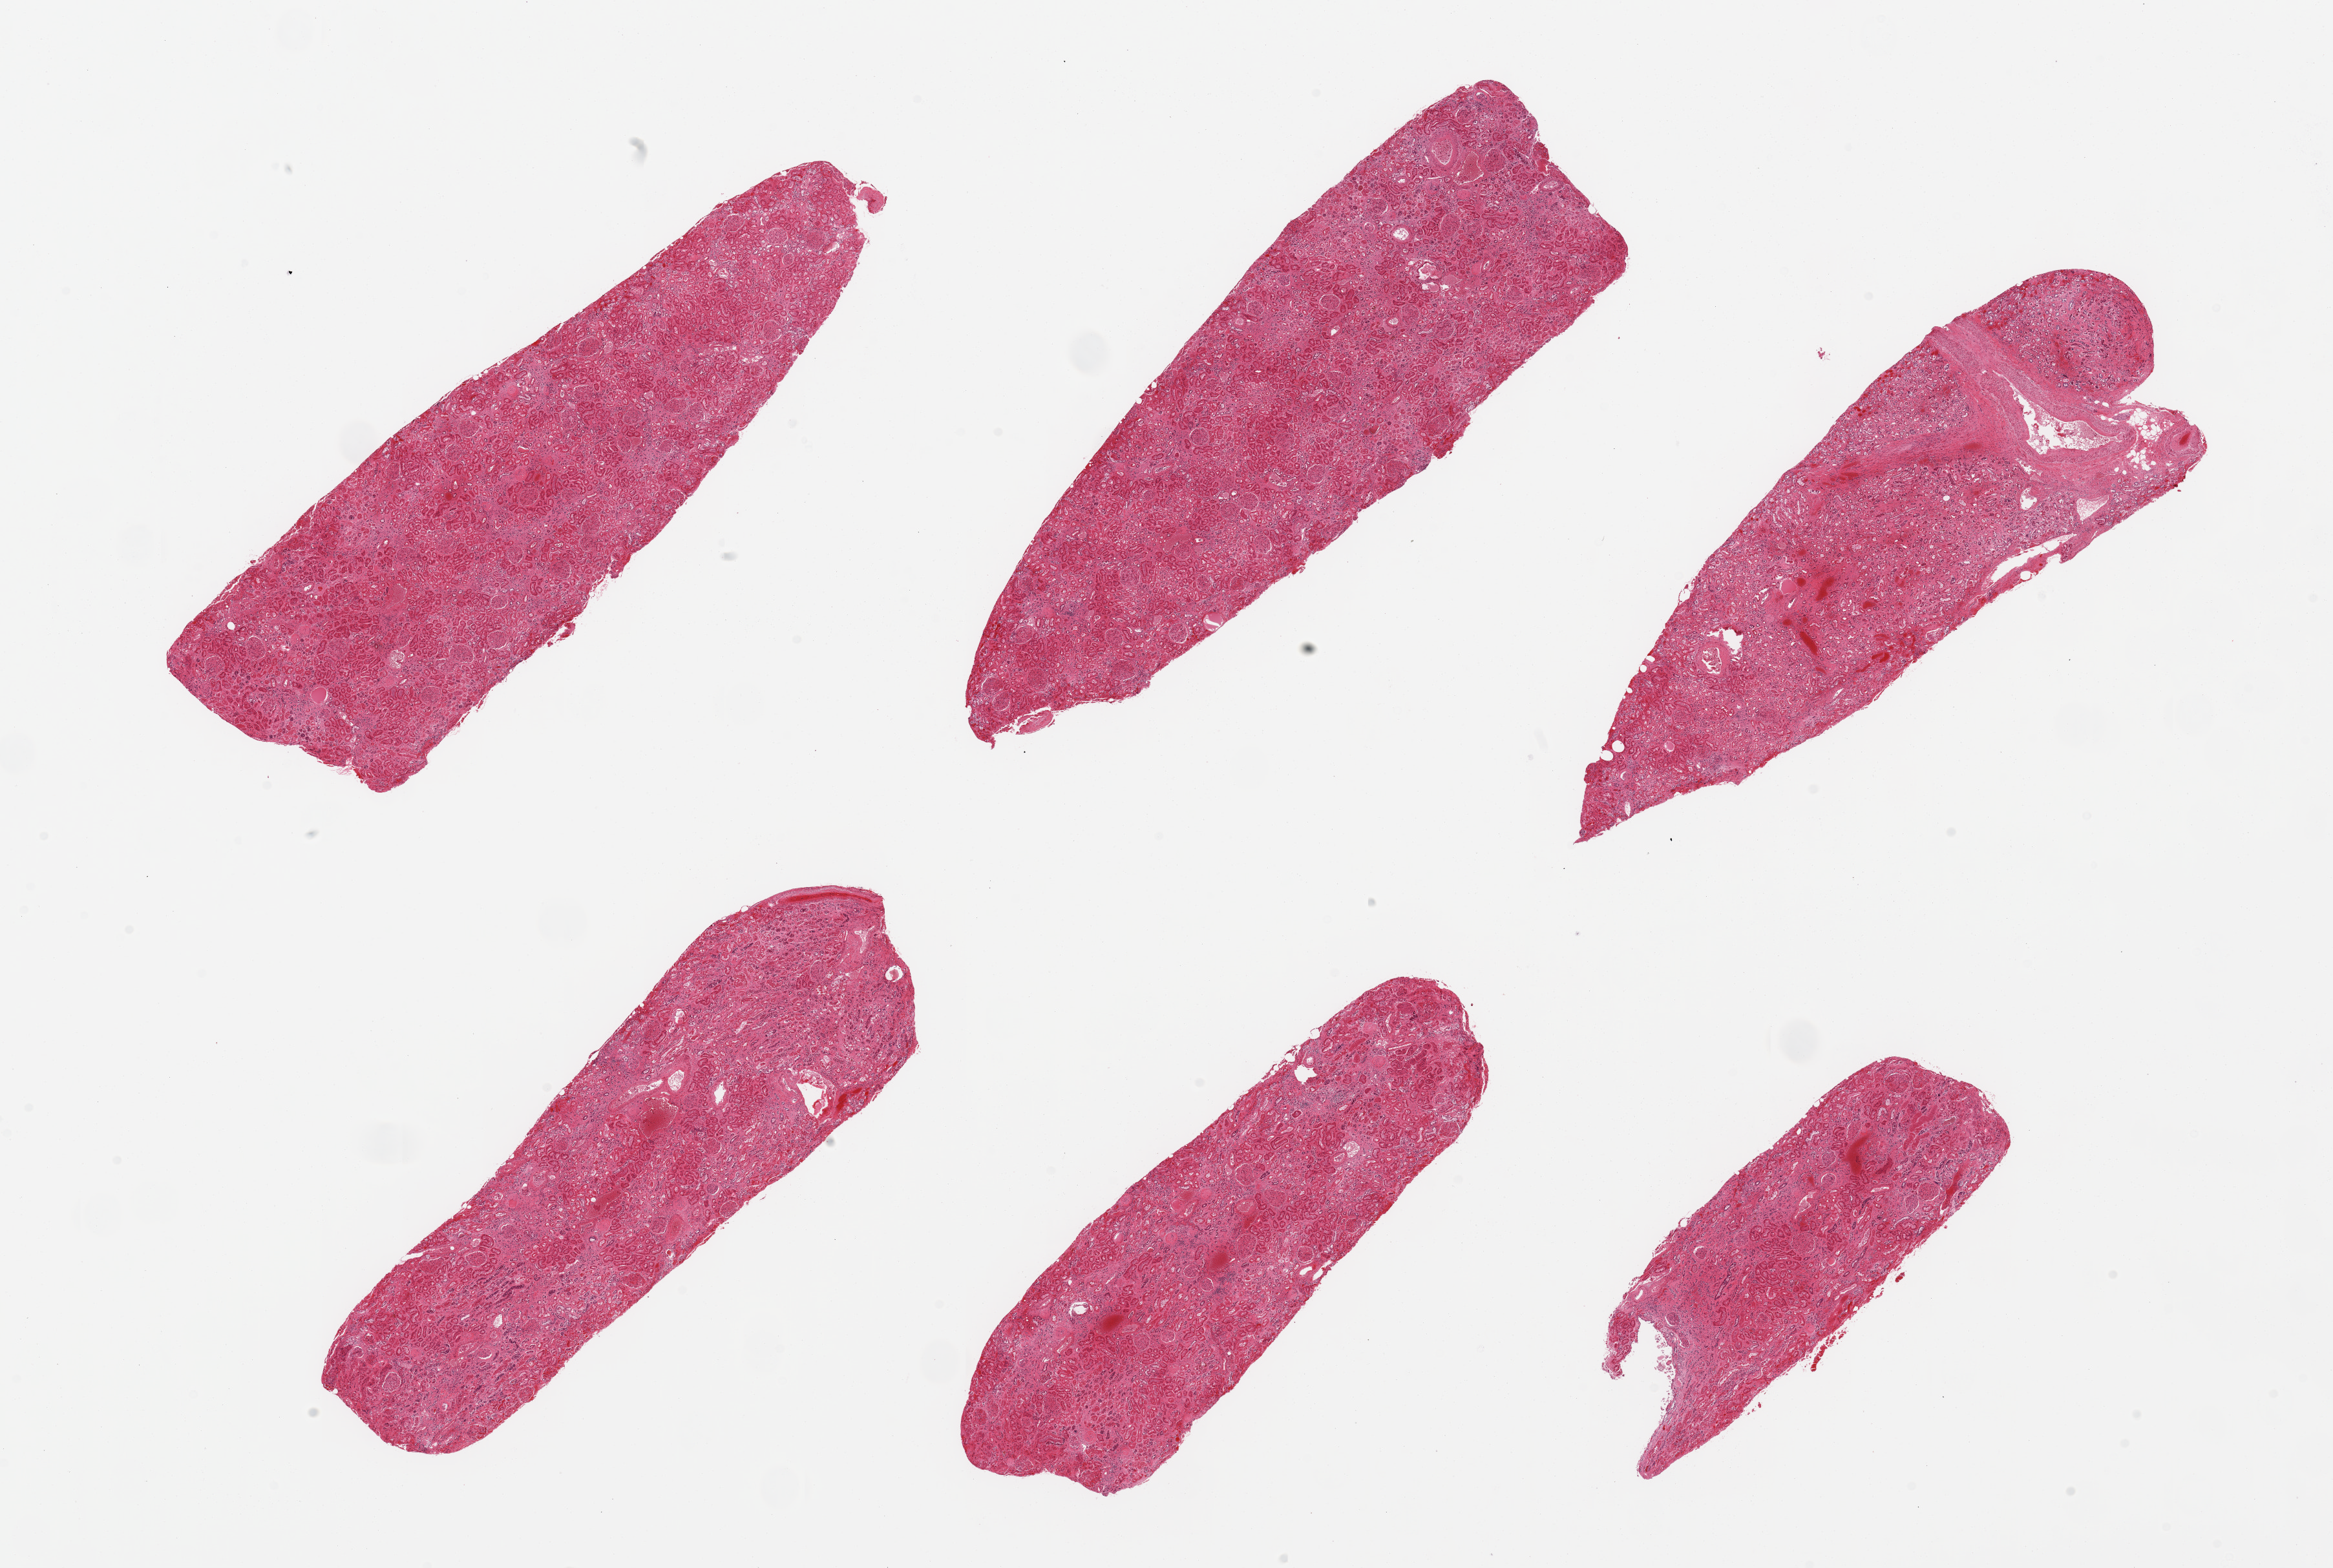
H&E whole-slide image — low-resolution overview of the scanned area, about 28.5 x 19.2 mm (slide scanned at 20x). PAXgene-fixed, paraffin-embedded tissue. Section of renal cortex (target tissue). Donor tissue sample. Donor sex: male.
- pathologist's review note for this sample: 6 pieces; scattered sclerosed glomeruli; 1 piece is mostly medulla